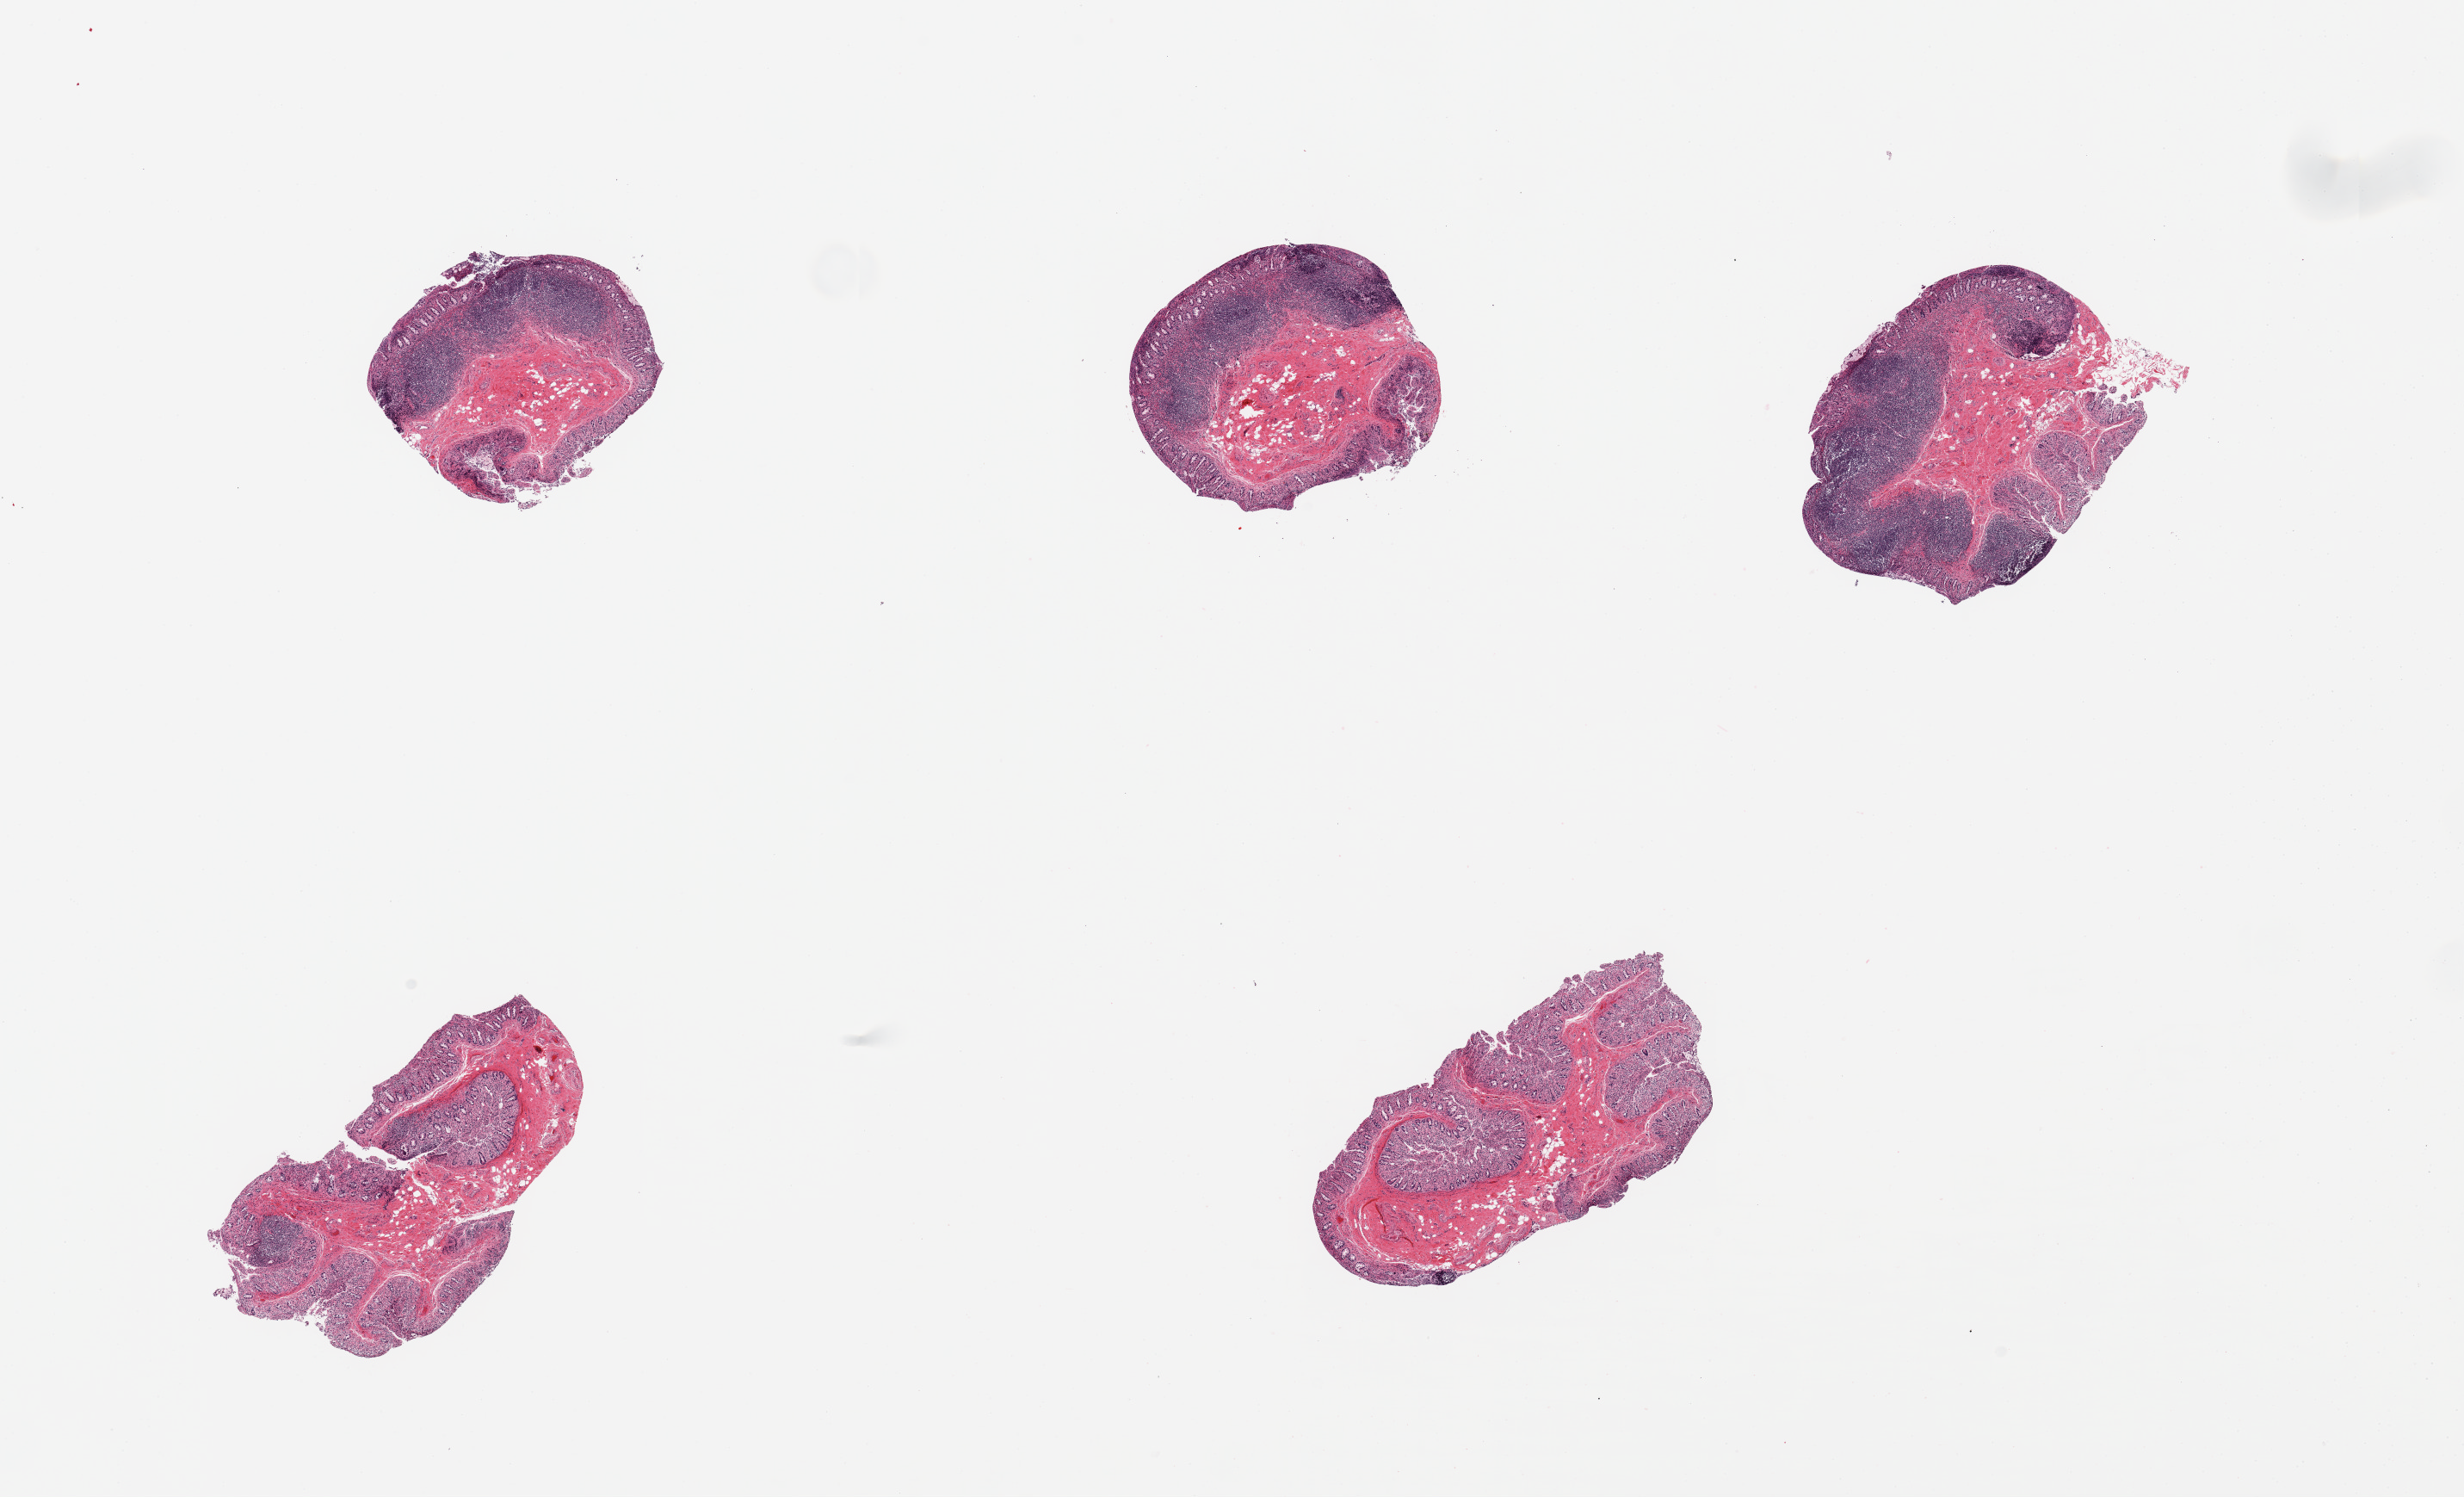
Digitized haematoxylin and eosin-stained section — shown as a low-resolution overview of the whole scanned area (about 22.6 x 13.8 mm, slide scanned at 20x); PAXgene-fixed, paraffin-embedded tissue; target tissue: ileum; tissue donor sample. Donor sex: male.
Reviewer comment on this tissue sample: 5 pieces; moderately autolyzed mucosa with several pieces with abundant lymphoid tissue.